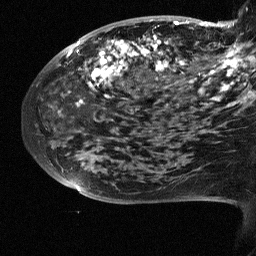
Breast MRI (dynamic contrast-enhanced), one sagittal slice. Slice 21 of 64 in the series (ordered by position). Dynamic contrast-enhanced study with each time point stored as its own series, time point 2 of 3 at this slice position (early post-contrast, ordered by acquisition time). 1.5 T. TE 4.5 ms, TR 11 ms. 2.5 mm slice thickness. 256 × 256 image matrix, field of view 200 × 200 mm. Female patient, age 38 years. From the clinical record (not read from this slice): setting: breast cancer imaged before/during neoadjuvant chemotherapy; receptor status: HR-positive, HER2-negative.
Outlined on this slice (semi-automatically segmented with operator editing):
- analysis volume of interest (the breast-tissue region the enhancement analysis was run in; not a lesion): box from (x=88, y=18) to (x=252, y=126) px
- tumour enhancement mask (voxels above the 90 % enhancement threshold inside the analysis volume of interest): (x=90, y=20)–(x=252, y=106)